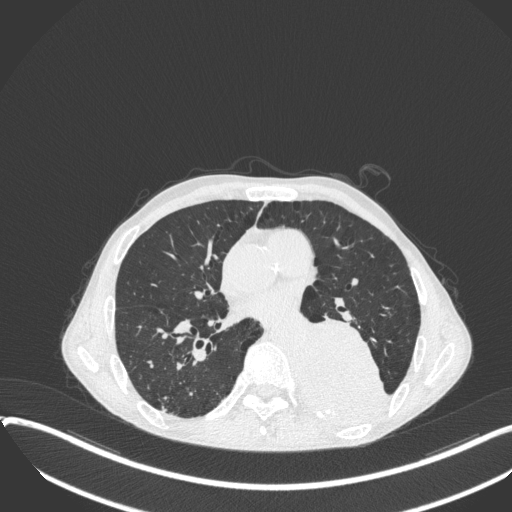
Chest CT, one axial slice. Slice 178 of 400 in the series (ordered by position). Reconstruction kernel B31f. 120 kVp. Lung window (W 1500 / L -600 HU). 512 × 512 image matrix. Male patient, age 57 years. From the clinical record (not read from this slice): clinical TNM (as recorded): T4 N0 M0.
Annotated regions visible in this slice (rectangle marked by the reading radiologist):
- lung tumour (recorded histology: squamous cell carcinoma): bounding box (x1, y1, x2, y2) in pixels: (299, 319, 392, 428)